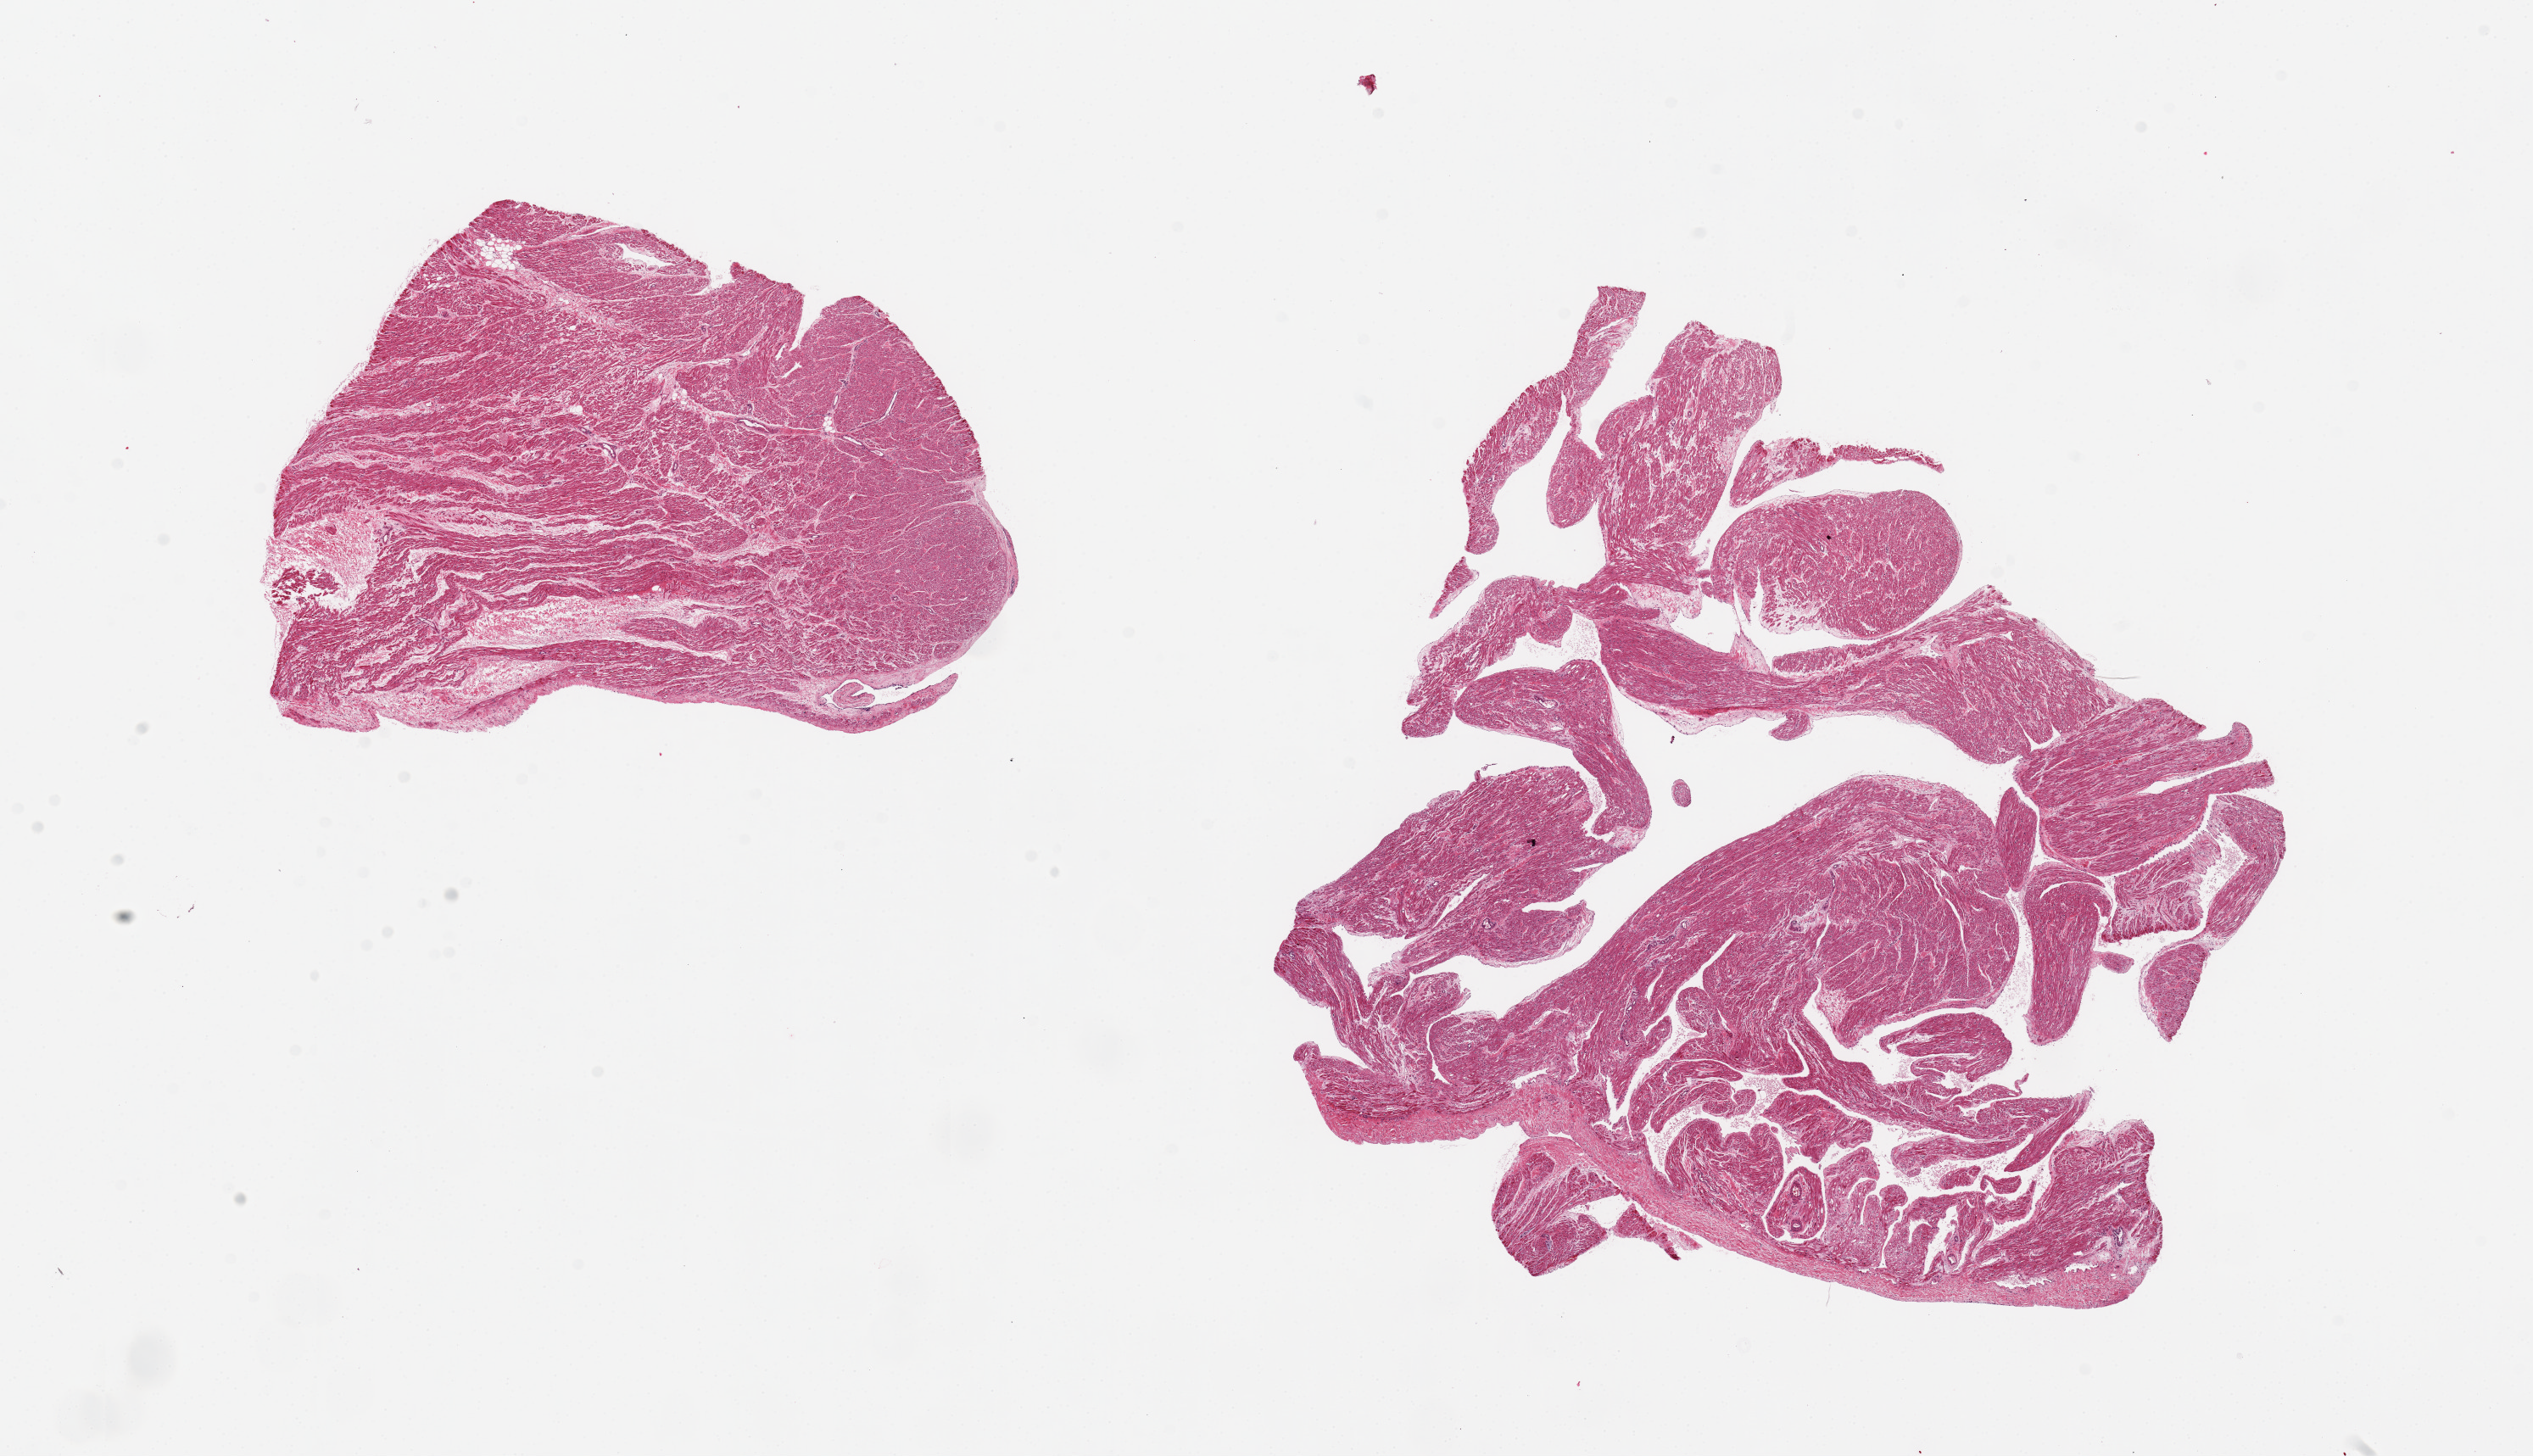
Haematoxylin and eosin whole-slide image — whole scanned area (about 23.6 x 13.6 mm) shown as a low-resolution overview. PAXgene-fixed paraffin-embedded (PFPE) section. Target tissue: auricular appendage. Tissue donor sample. Donor: male.
* reviewer comment on this tissue sample: 2 pieces, 8x8 and 6x5.5mm